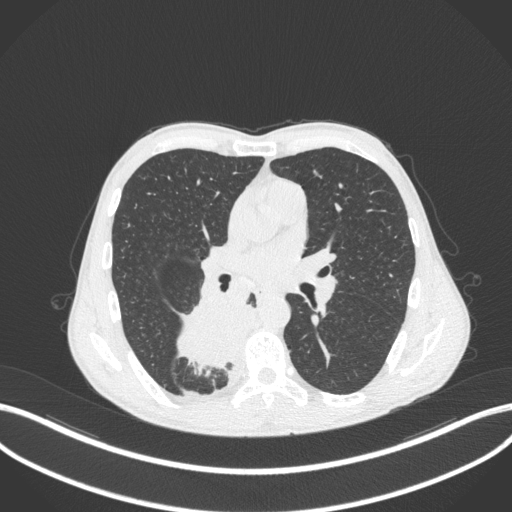
Chest CT, one axial slice; slice 203 of 371 in the series (ordered by position); reconstruction kernel B31f; 120 kVp; lung window (W 1500 / L -600 HU); 512 × 512 image matrix. Male patient, age 58 years. From the clinical record (not read from this slice): clinical TNM (as recorded): T3 N1 M1.
Structures marked on this image (rectangle marked by the reading radiologist):
- lung tumour (recorded histology: squamous cell carcinoma): bounding box (x1, y1, x2, y2) in pixels: (166, 288, 256, 373)